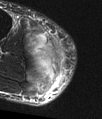
MRI of an extremity soft-tissue mass, one axial slice; position 34 of 48 along the scan axis; T2-weighted fat-saturated; MR volume resampled by the dataset authors to the PET/CT grid (not the native acquisition matrix); 102 × 119 image matrix. Male patient. From the clinical record (not read from this slice): histological type: pleiomorphic liposarcoma; grade: high; site of the primary tumour: right calf.
Structures marked on this image (expert contour drawn on MRI and transferred to this co-registered scan by the dataset authors):
- gross tumour volume including surrounding oedema: bounding box (x1, y1, x2, y2) in pixels: (26, 33, 65, 81)
- gross tumour volume (mass): (37, 42, 61, 74)